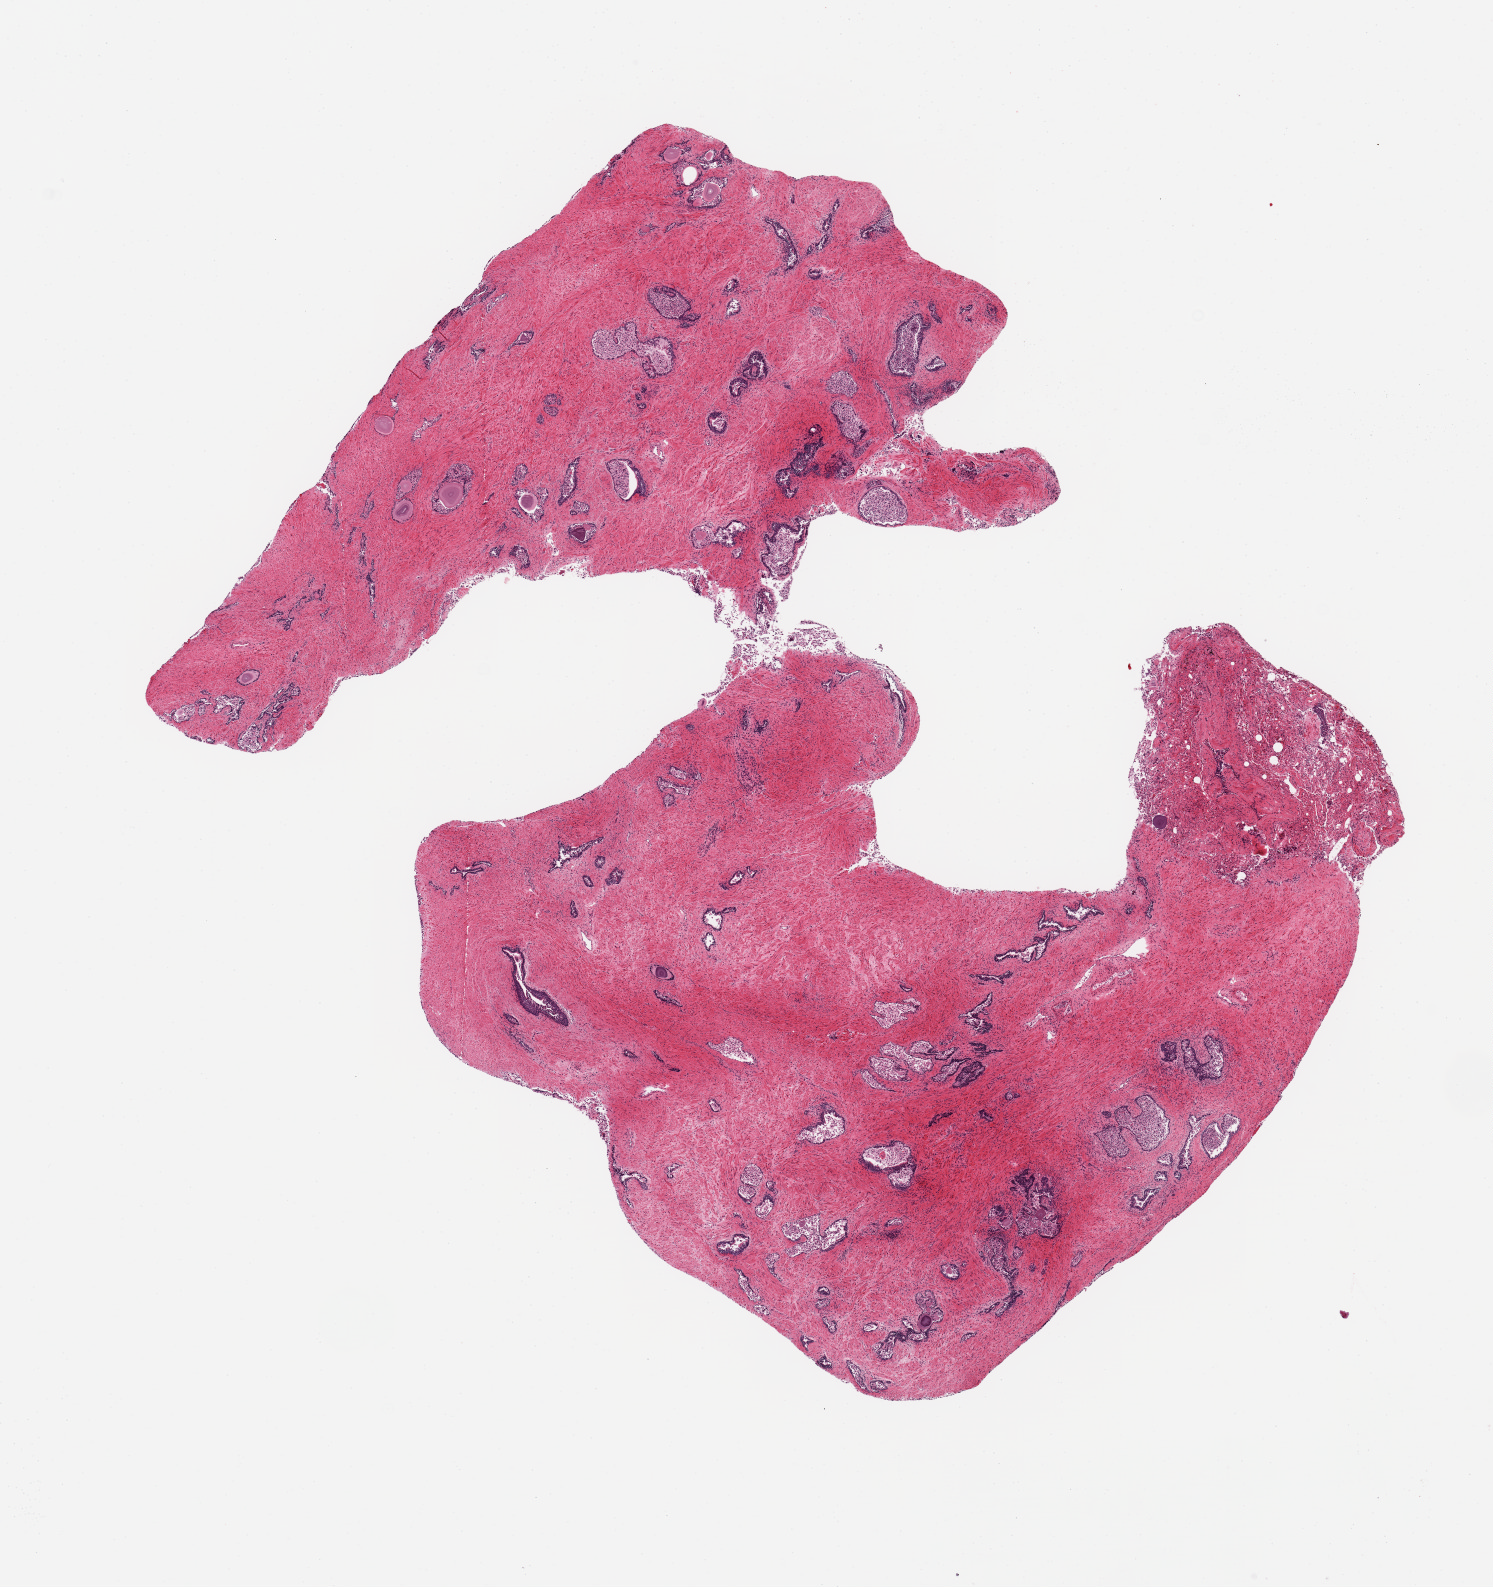
Hematoxylin and eosin (H&E) whole-slide image, brightfield — shown as a low-resolution overview of the whole scanned area (about 11.8 x 12.6 mm), PAXgene-fixed paraffin-embedded (PFPE) section, target tissue: prostate, donor tissue sample. Donor sex: male.
Pathologist's review note for this sample: 2 pieces, glandular component badly autolyzed.